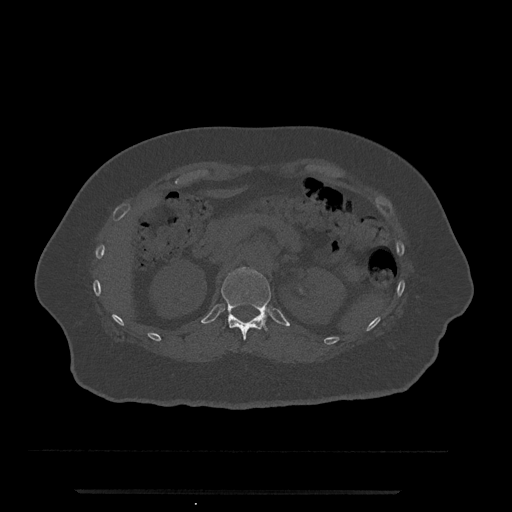
CT including the spine, one axial slice; position 164 of 797 along the scan axis; 120 kVp; bone window (W 1800 / L 400 HU); 512 × 512 image matrix. Patient: female, 51 years. From the clinical record (not read from this slice): primary cancer: neuro.
Structures marked on this image (semi-automatically segmented with operator editing):
- T12 vertebra: bounding box <221,267,271,340> (left, top, right, bottom; pixels)